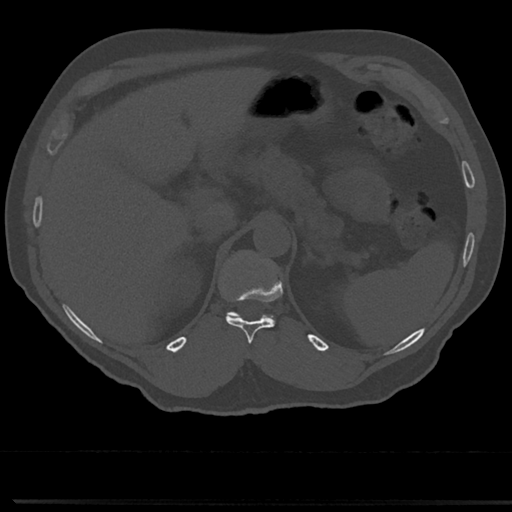
CT including the spine, one axial slice; position 185 of 817 along the scan axis; 120 kVp; bone window (W 1800 / L 400 HU); 0.5 mm slice thickness; 512 × 512 image matrix, field of view 355 × 355 mm. Patient: male, 61 years. Case-level facts recorded for this patient, not image findings: primary cancer: prostate.
Outlined on this slice (semi-automatic segmentation, software-assisted and operator-edited):
- T11 vertebra: box from (x=226, y=289) to (x=281, y=345) px
- T12 vertebra: (x=225, y=251)–(x=276, y=320)